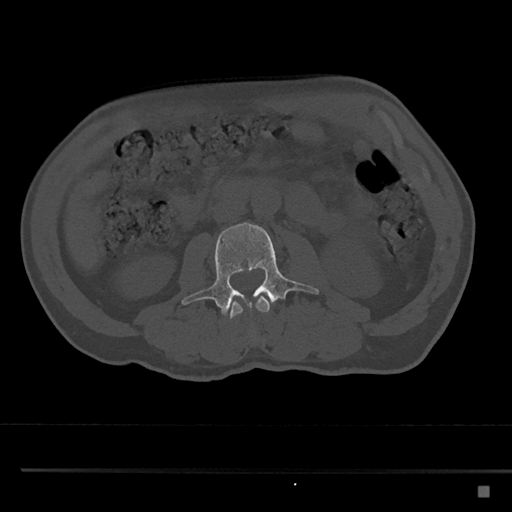
CT including the spine, one axial slice; slice 709 of 797 in the series (ordered by position); 120 kVp; bone window (W 1800 / L 400 HU); 0.5 mm slice thickness; 512 × 512 image matrix. Male patient, age 59 years. From the clinical record (not read from this slice): primary cancer: prostate.
Annotated regions visible in this slice (semi-automatically segmented with operator editing):
- L2 vertebra: box from (x=228, y=296) to (x=270, y=319) px
- L3 vertebra: (x=181, y=222)–(x=319, y=316)